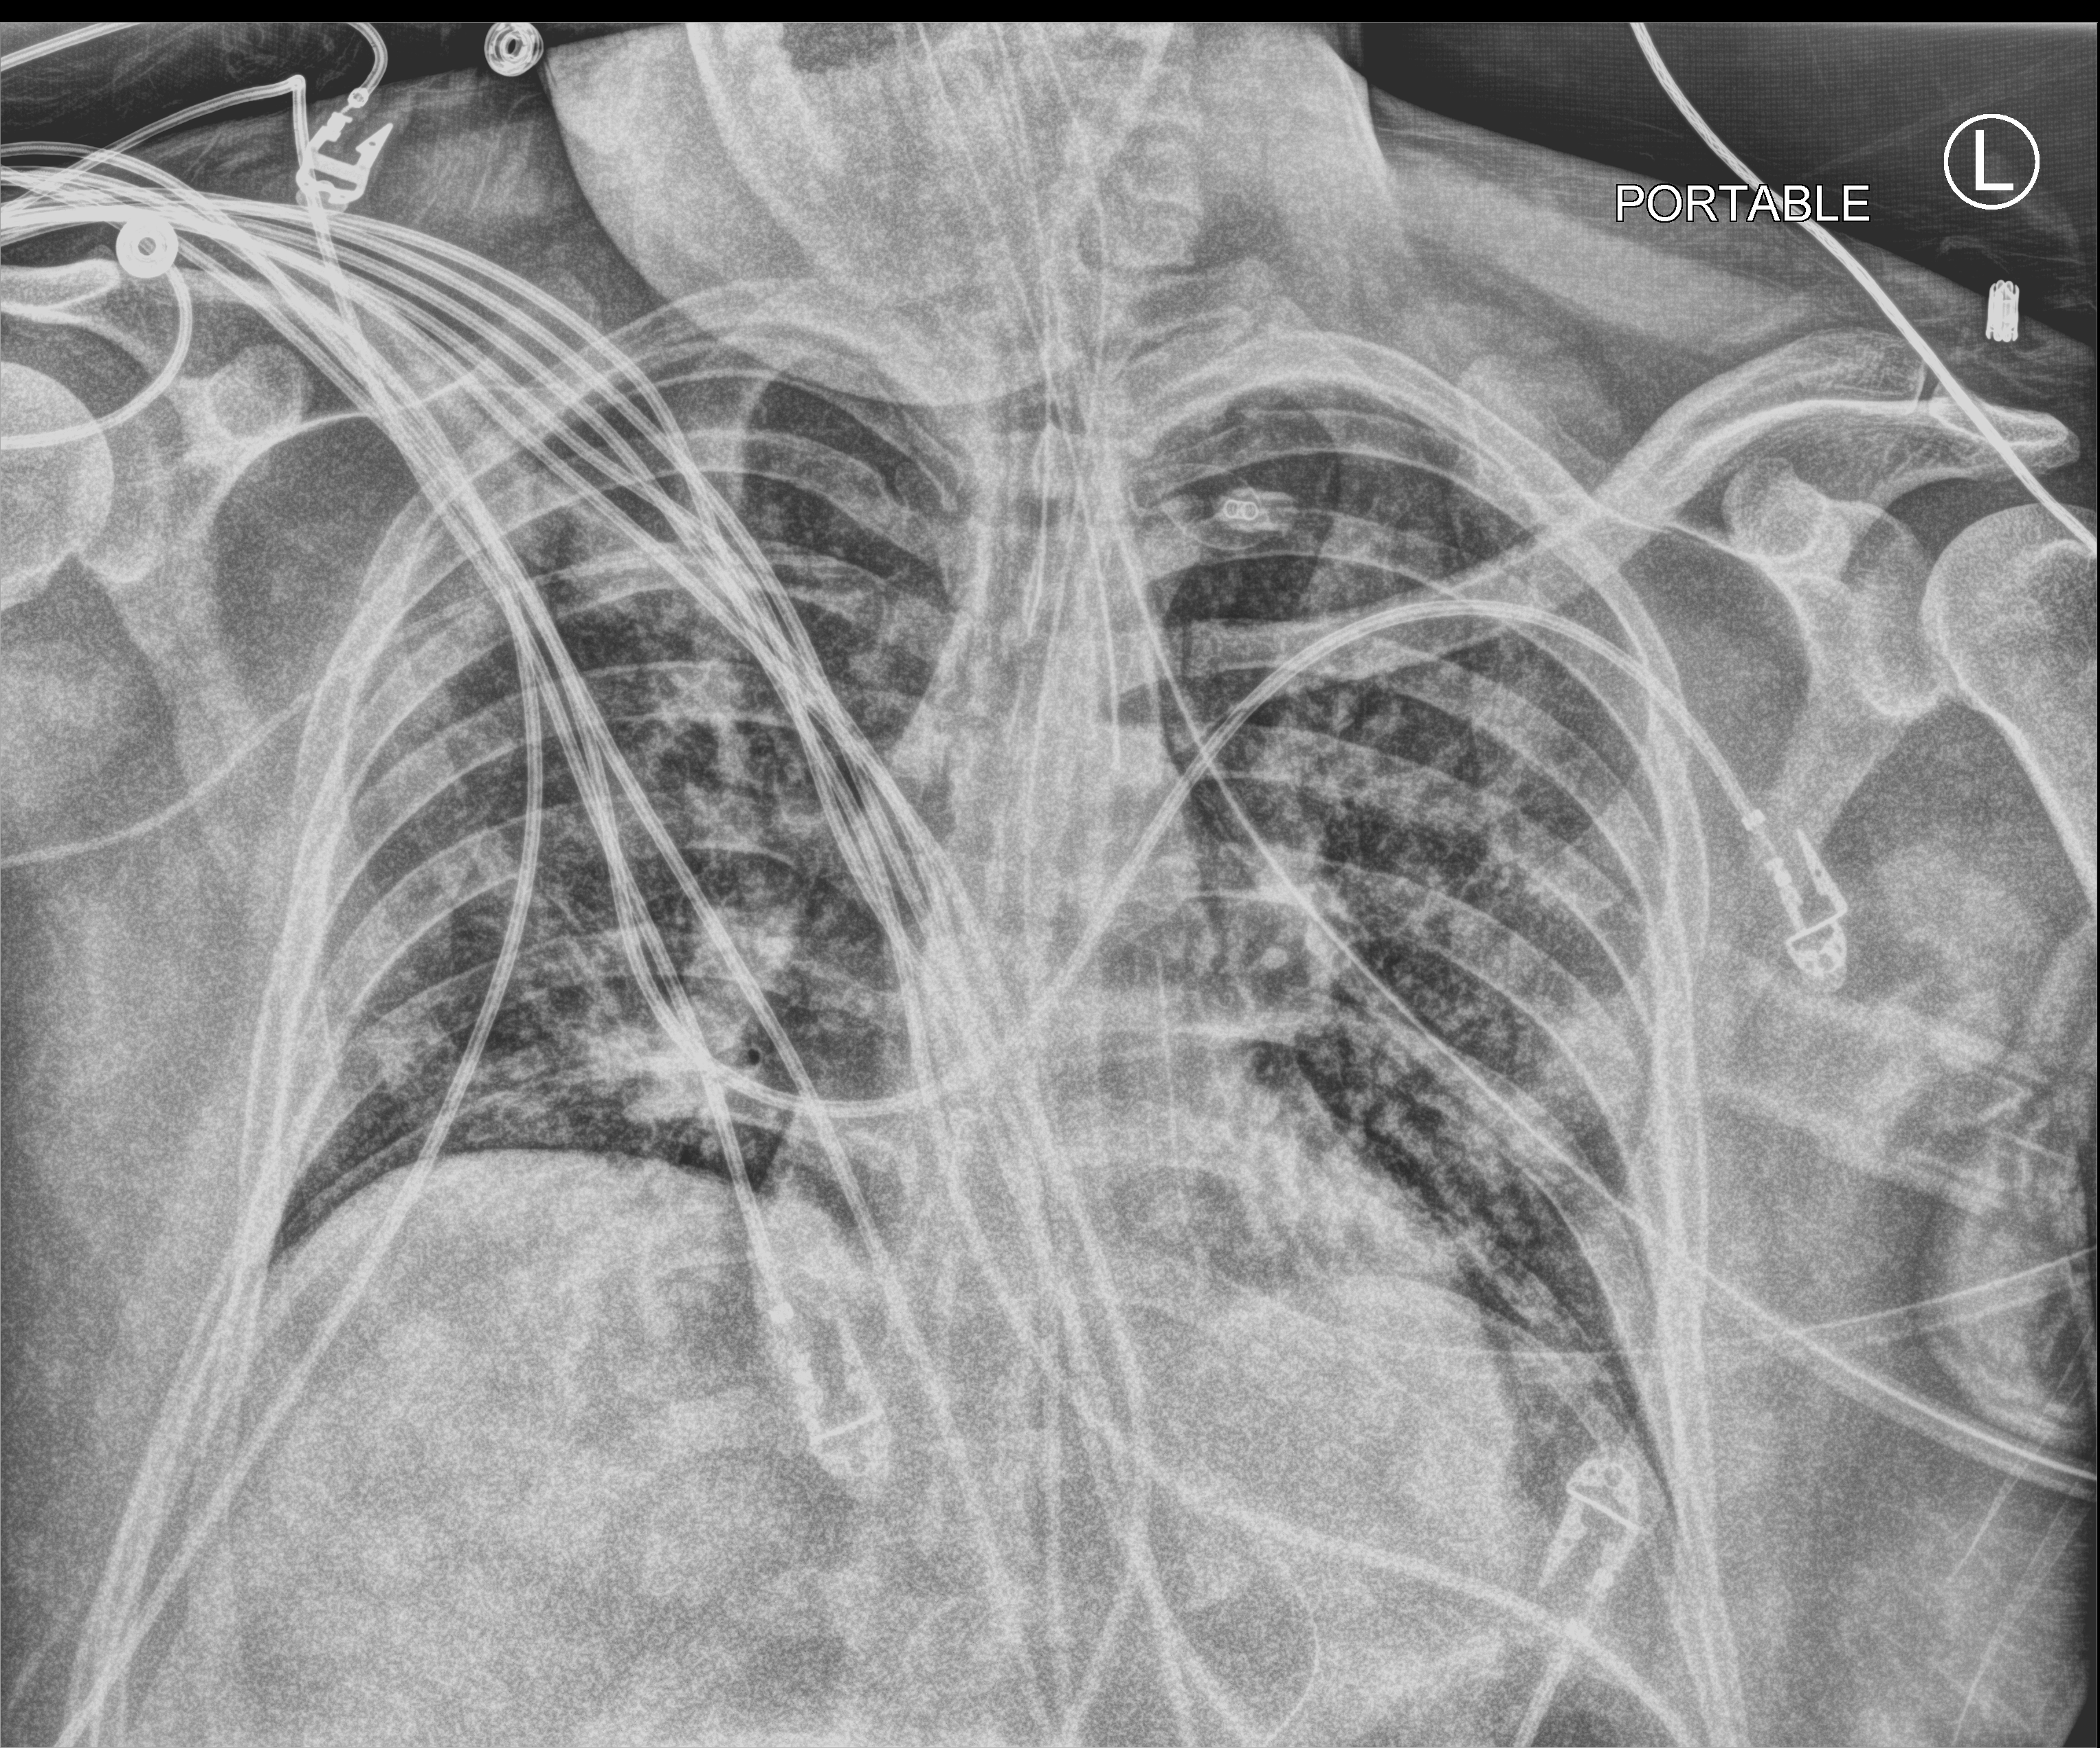
Bedside chest radiograph (computed radiography), anteroposterior (AP) projection. Male patient hospitalised with COVID-19, age 18–59 years.
Hospital-stay facts (about this admission, not read from this image; timing relative to this image not recorded): admitted to intensive care during this hospital stay: yes; smoking status (admission record): never.